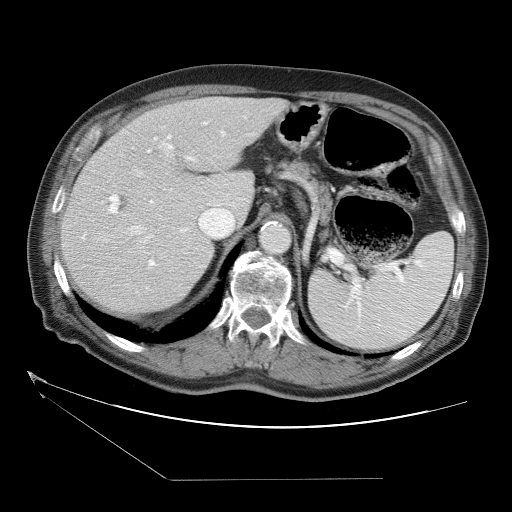
Contrast-enhanced abdominal CT (liver protocol), one axial slice. Slice 23 of 38 in the series (ordered by position). One of 2 acquisitions stored at this slice position. Soft-tissue window (W 400 / L 40 HU). 5 mm slice thickness. 512 × 512 image matrix, field of view 400 × 400 mm. Case-level facts recorded for this patient, not image findings: diagnosis: hepatocellular carcinoma (patient treated with transarterial chemoembolisation; whether this scan precedes or follows treatment is not stated here); TNM stage (as recorded): Stage-II; Child-Pugh class: A.
Structures marked on this image (semi-automatically segmented with operator editing):
- abdominal aorta: bounding box <262,225,291,253> (left, top, right, bottom; pixels)
- liver parenchyma outside the tumour (the mass and vessels are separate outlines, so this box may not span the whole liver): <60,96,288,314>
- liver vessels: <82,121,226,304>